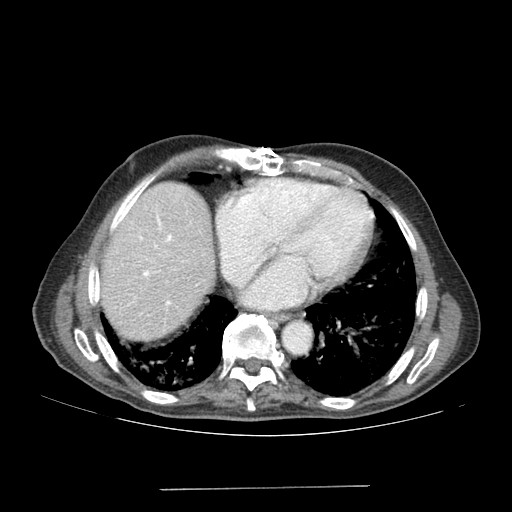
Contrast-enhanced abdominal CT (liver protocol), one axial slice; position 162 of 192 along the scan axis; soft-tissue window (W 400 / L 40 HU); 2.5 mm slice thickness; 512 × 512 image matrix, field of view 400 × 400 mm. Case-level facts recorded for this patient, not image findings: diagnosis: hepatocellular carcinoma (patient treated with transarterial chemoembolisation; whether this scan precedes or follows treatment is not stated here); TNM stage (as recorded): Stage-IVA; Child-Pugh class: A; tumour differentiation: poorly differentiated; tumour nodularity: uninodular.
Outlined on this slice (semi-automatic segmentation, software-assisted and operator-edited):
- liver parenchyma outside the tumour (the mass and vessels are separate outlines, so this box may not span the whole liver): bounding box [x1, y1, x2, y2] px = [100, 182, 214, 340]
- liver vessels: [118, 216, 172, 305]